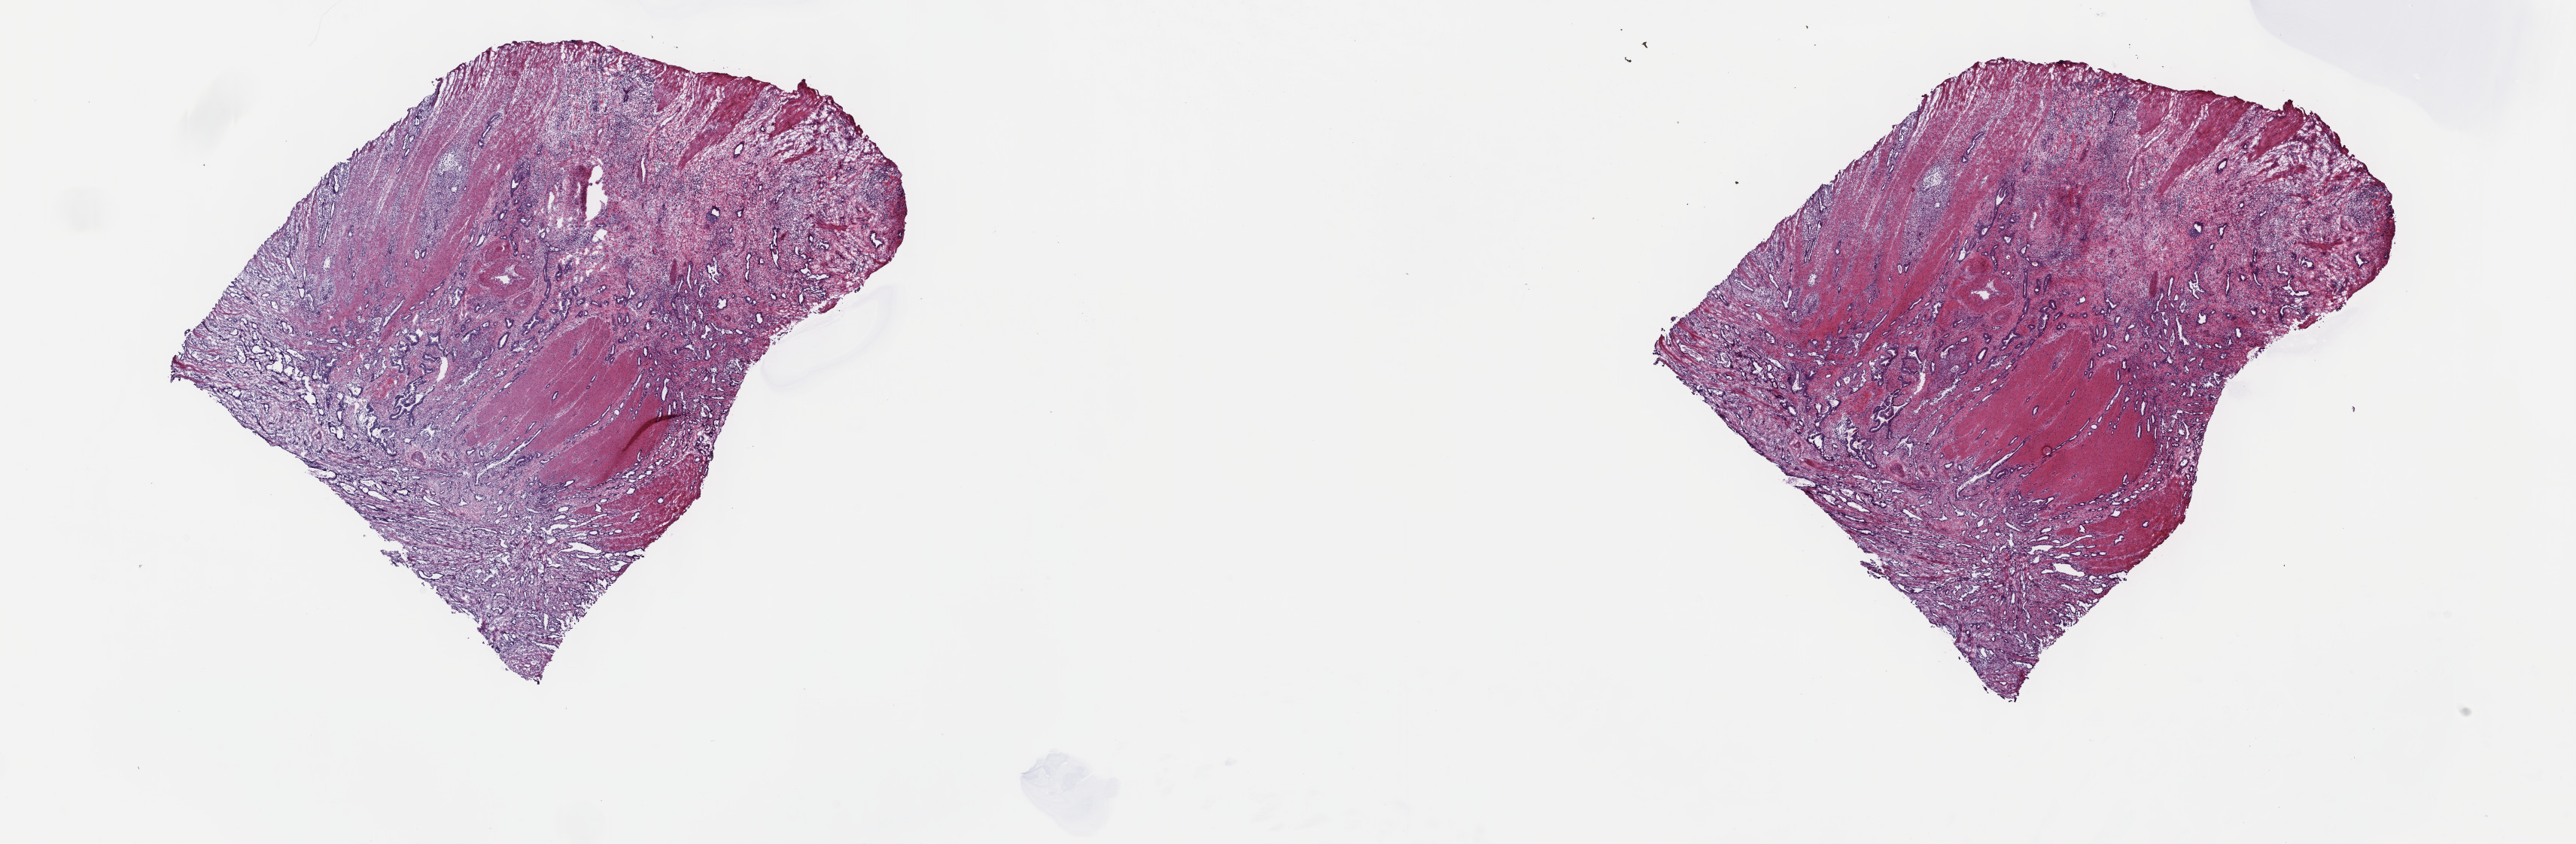
Digitized H&E-stained tissue section (whole slide) — shown as a low-resolution overview of the whole scanned area (about 27.7 x 9.1 mm), frozen section, pancreas, primary tumour sample. Patient: female, age at initial diagnosis 72 years. Histologic grade: G2 (moderately differentiated). Slide review estimates, as recorded: tumour cells 100%, tumour nuclei 60%, normal cells 0%, stromal cells 0%, necrosis 0%. Infiltration values recorded for this section: lymphocyte infiltration 5%, monocyte infiltration 0%, neutrophil infiltration 0%.
AJCC pathologic stage: IIB. Lymph nodes positive (case pathology): 1 of 21 examined. Histologic diagnosis: Infiltrating duct carcinoma, NOS (head of pancreas).